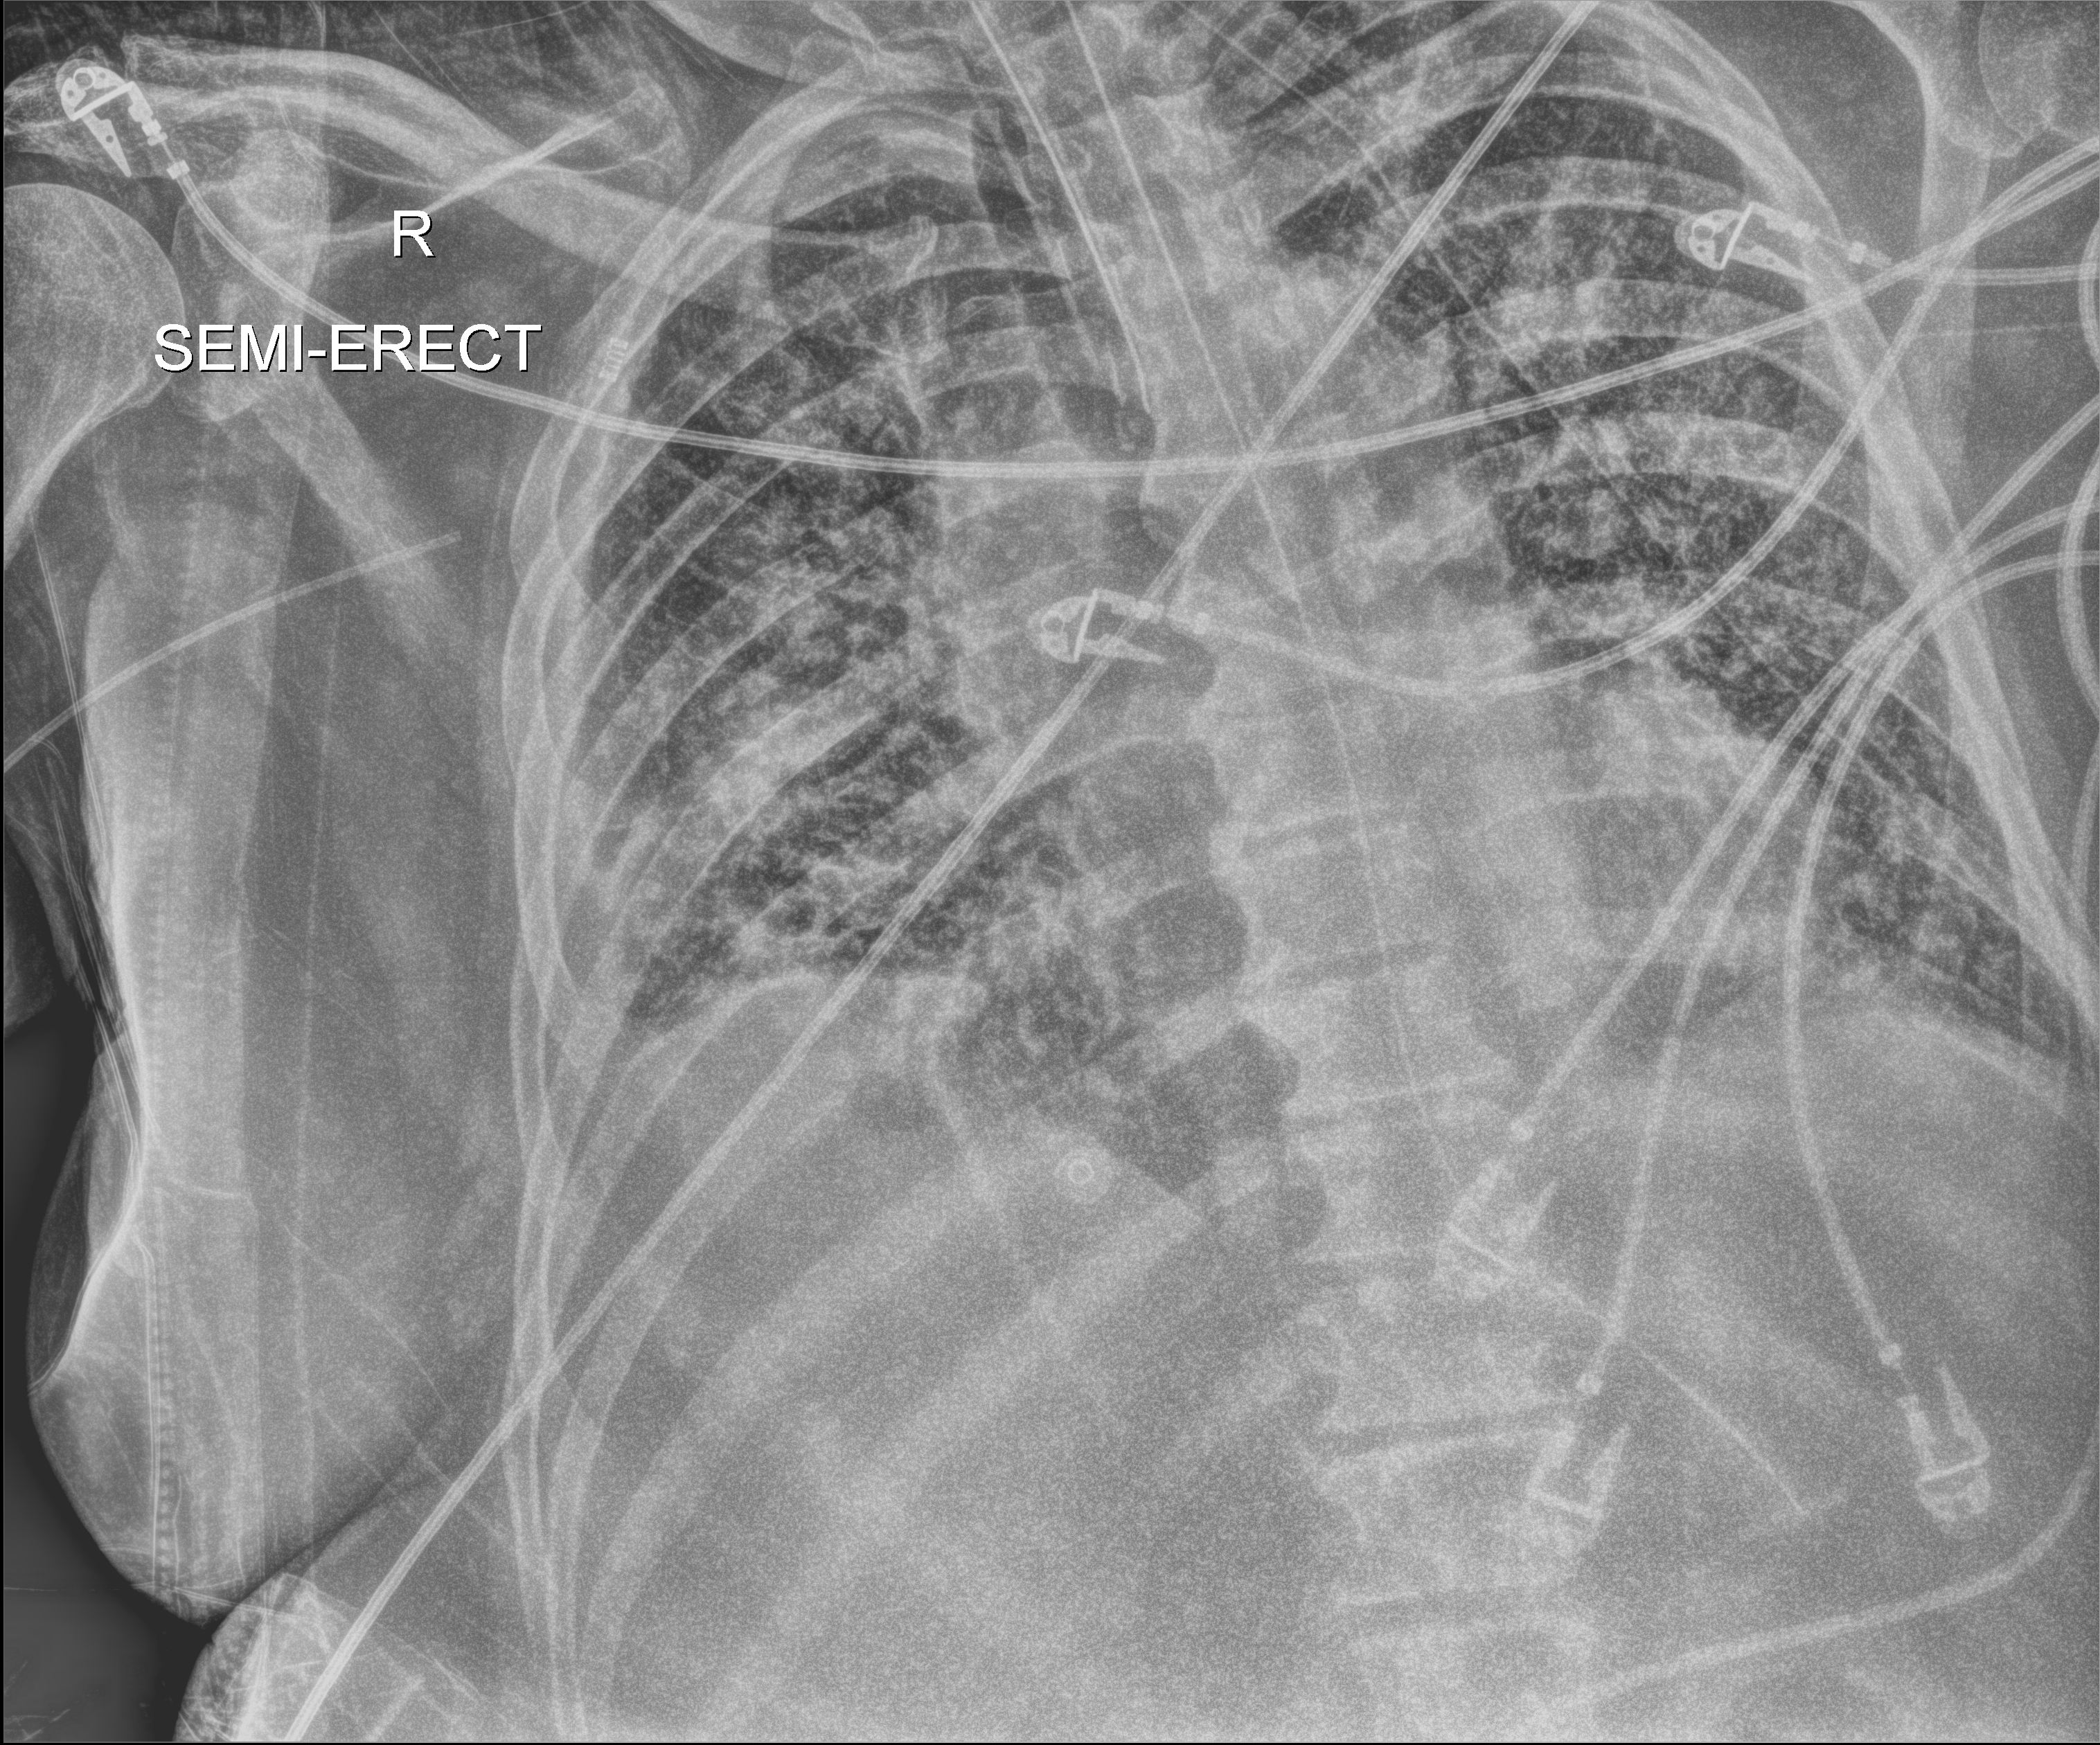
Bedside chest radiograph (digital radiography), anteroposterior (AP) projection. Male patient hospitalised with COVID-19, age 60–74 years.
Hospital-stay facts (about this admission, not read from this image; timing relative to this image not recorded): length of hospital stay: 40 days; diabetes (admission record): no.